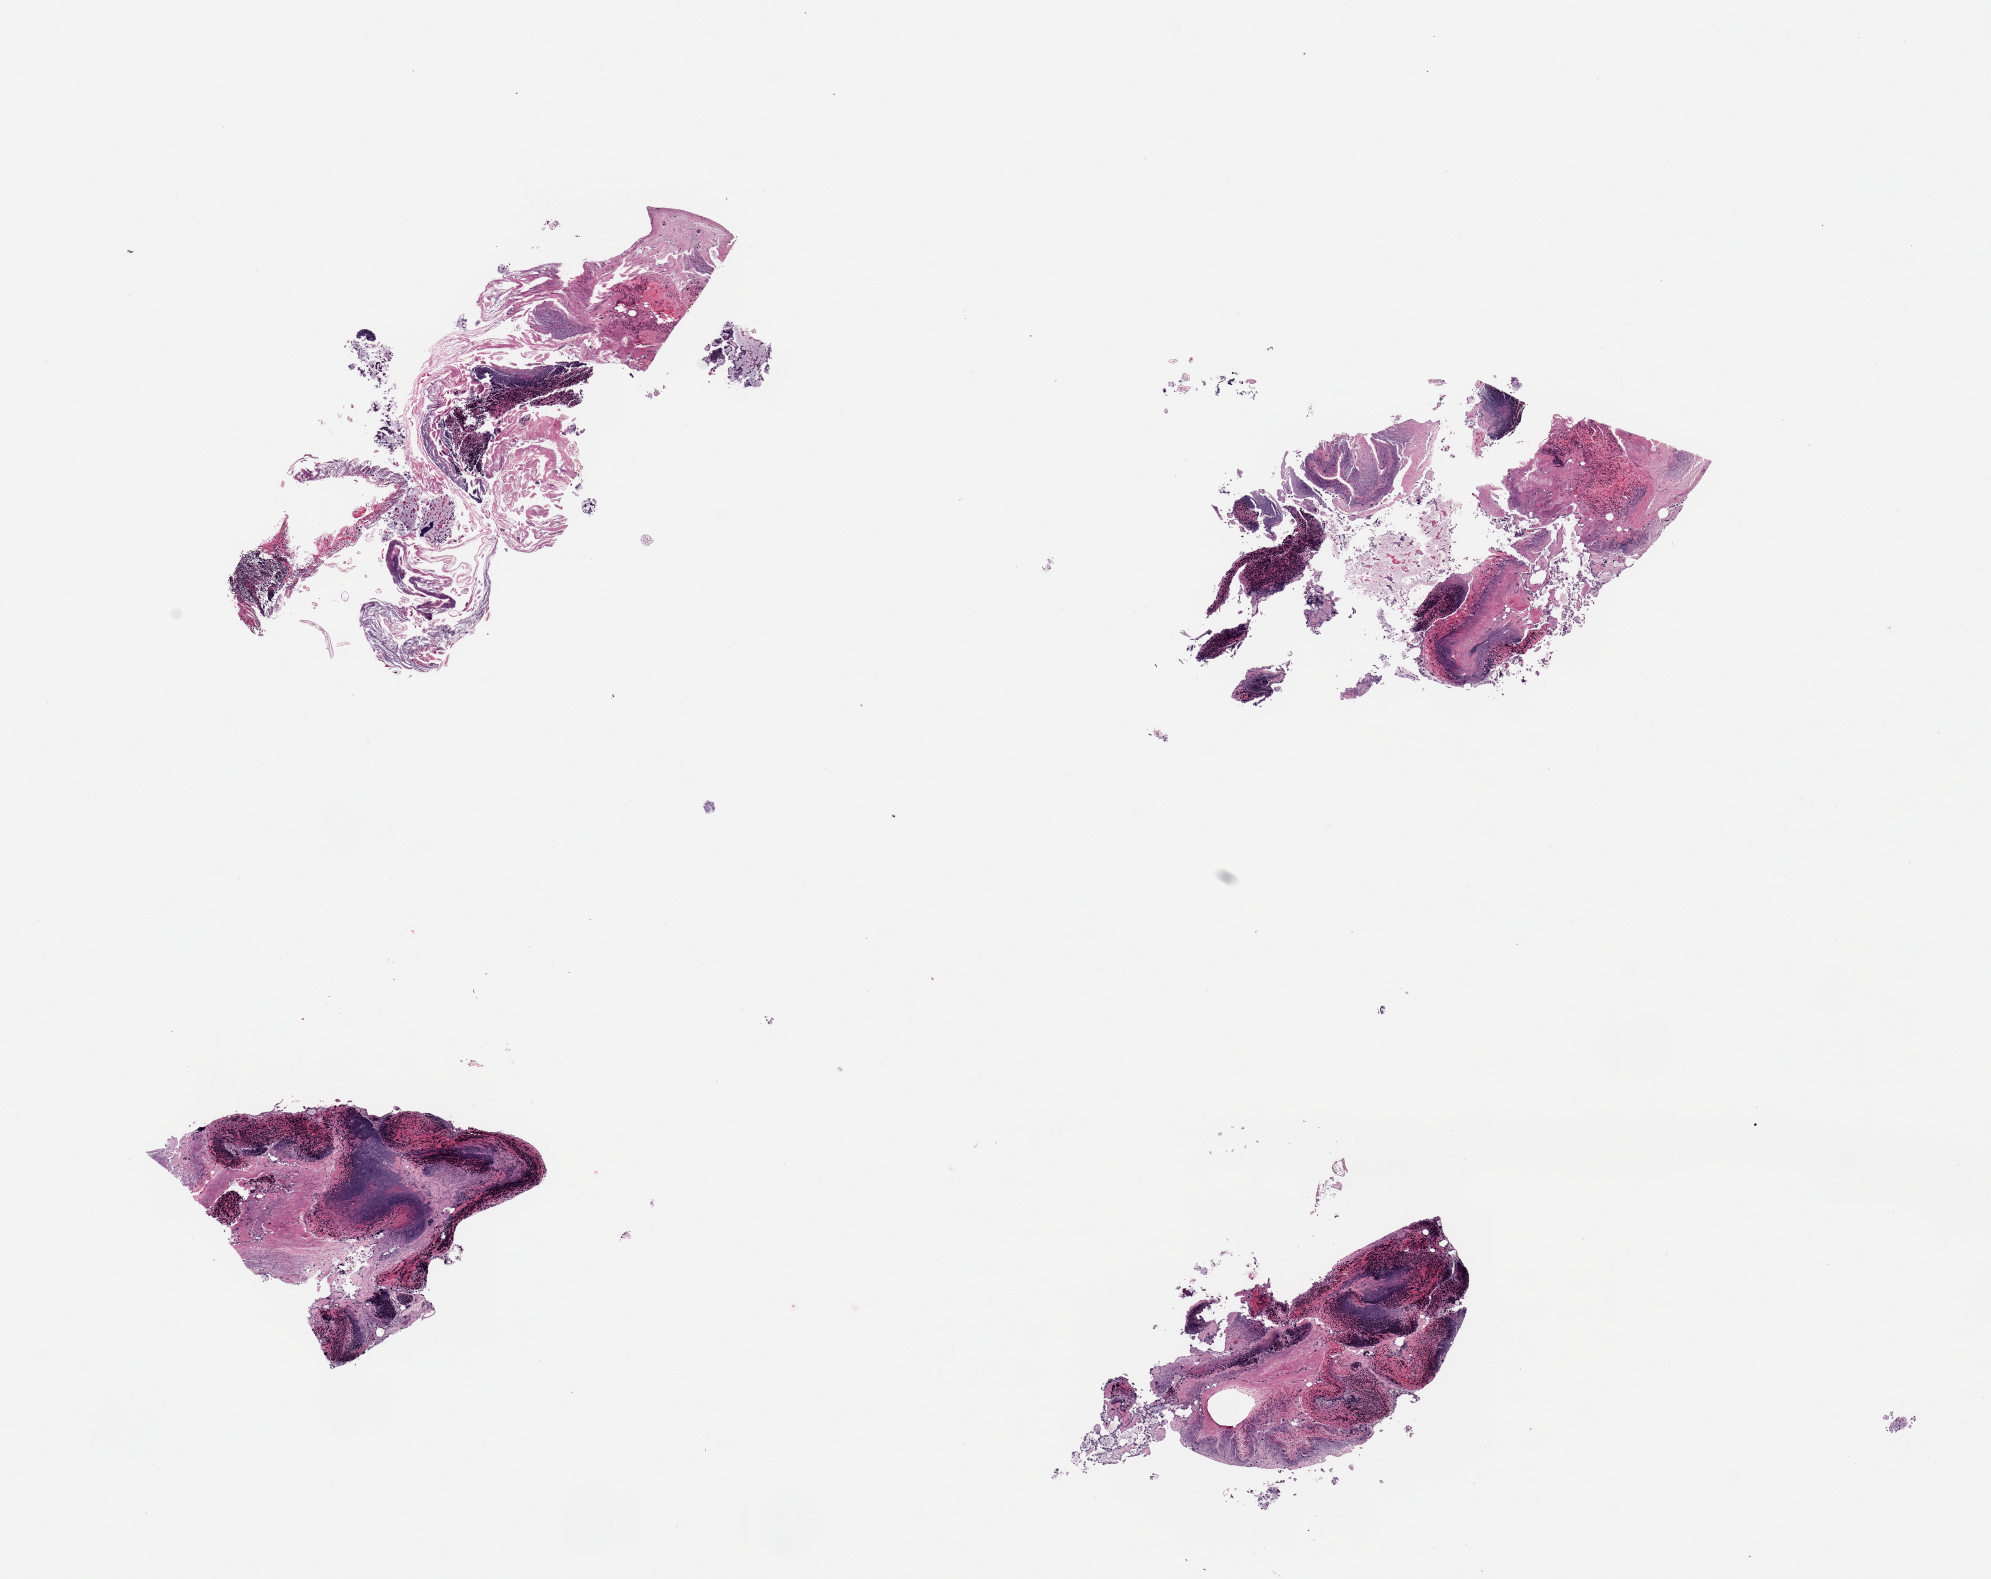
Whole-slide image, hematoxylin and eosin (H&E) stain, a low-resolution overview of the entire scanned area, about 15.8 x 12.5 mm (acquisition: 20x scan); PAXgene-fixed paraffin-embedded (PFPE) section; sampled site (target tissue): ileum; donor tissue sample. Male donor.
Reviewer comment on this tissue sample: 4 pieces; abundant but autolyzed lymphoid tissue.